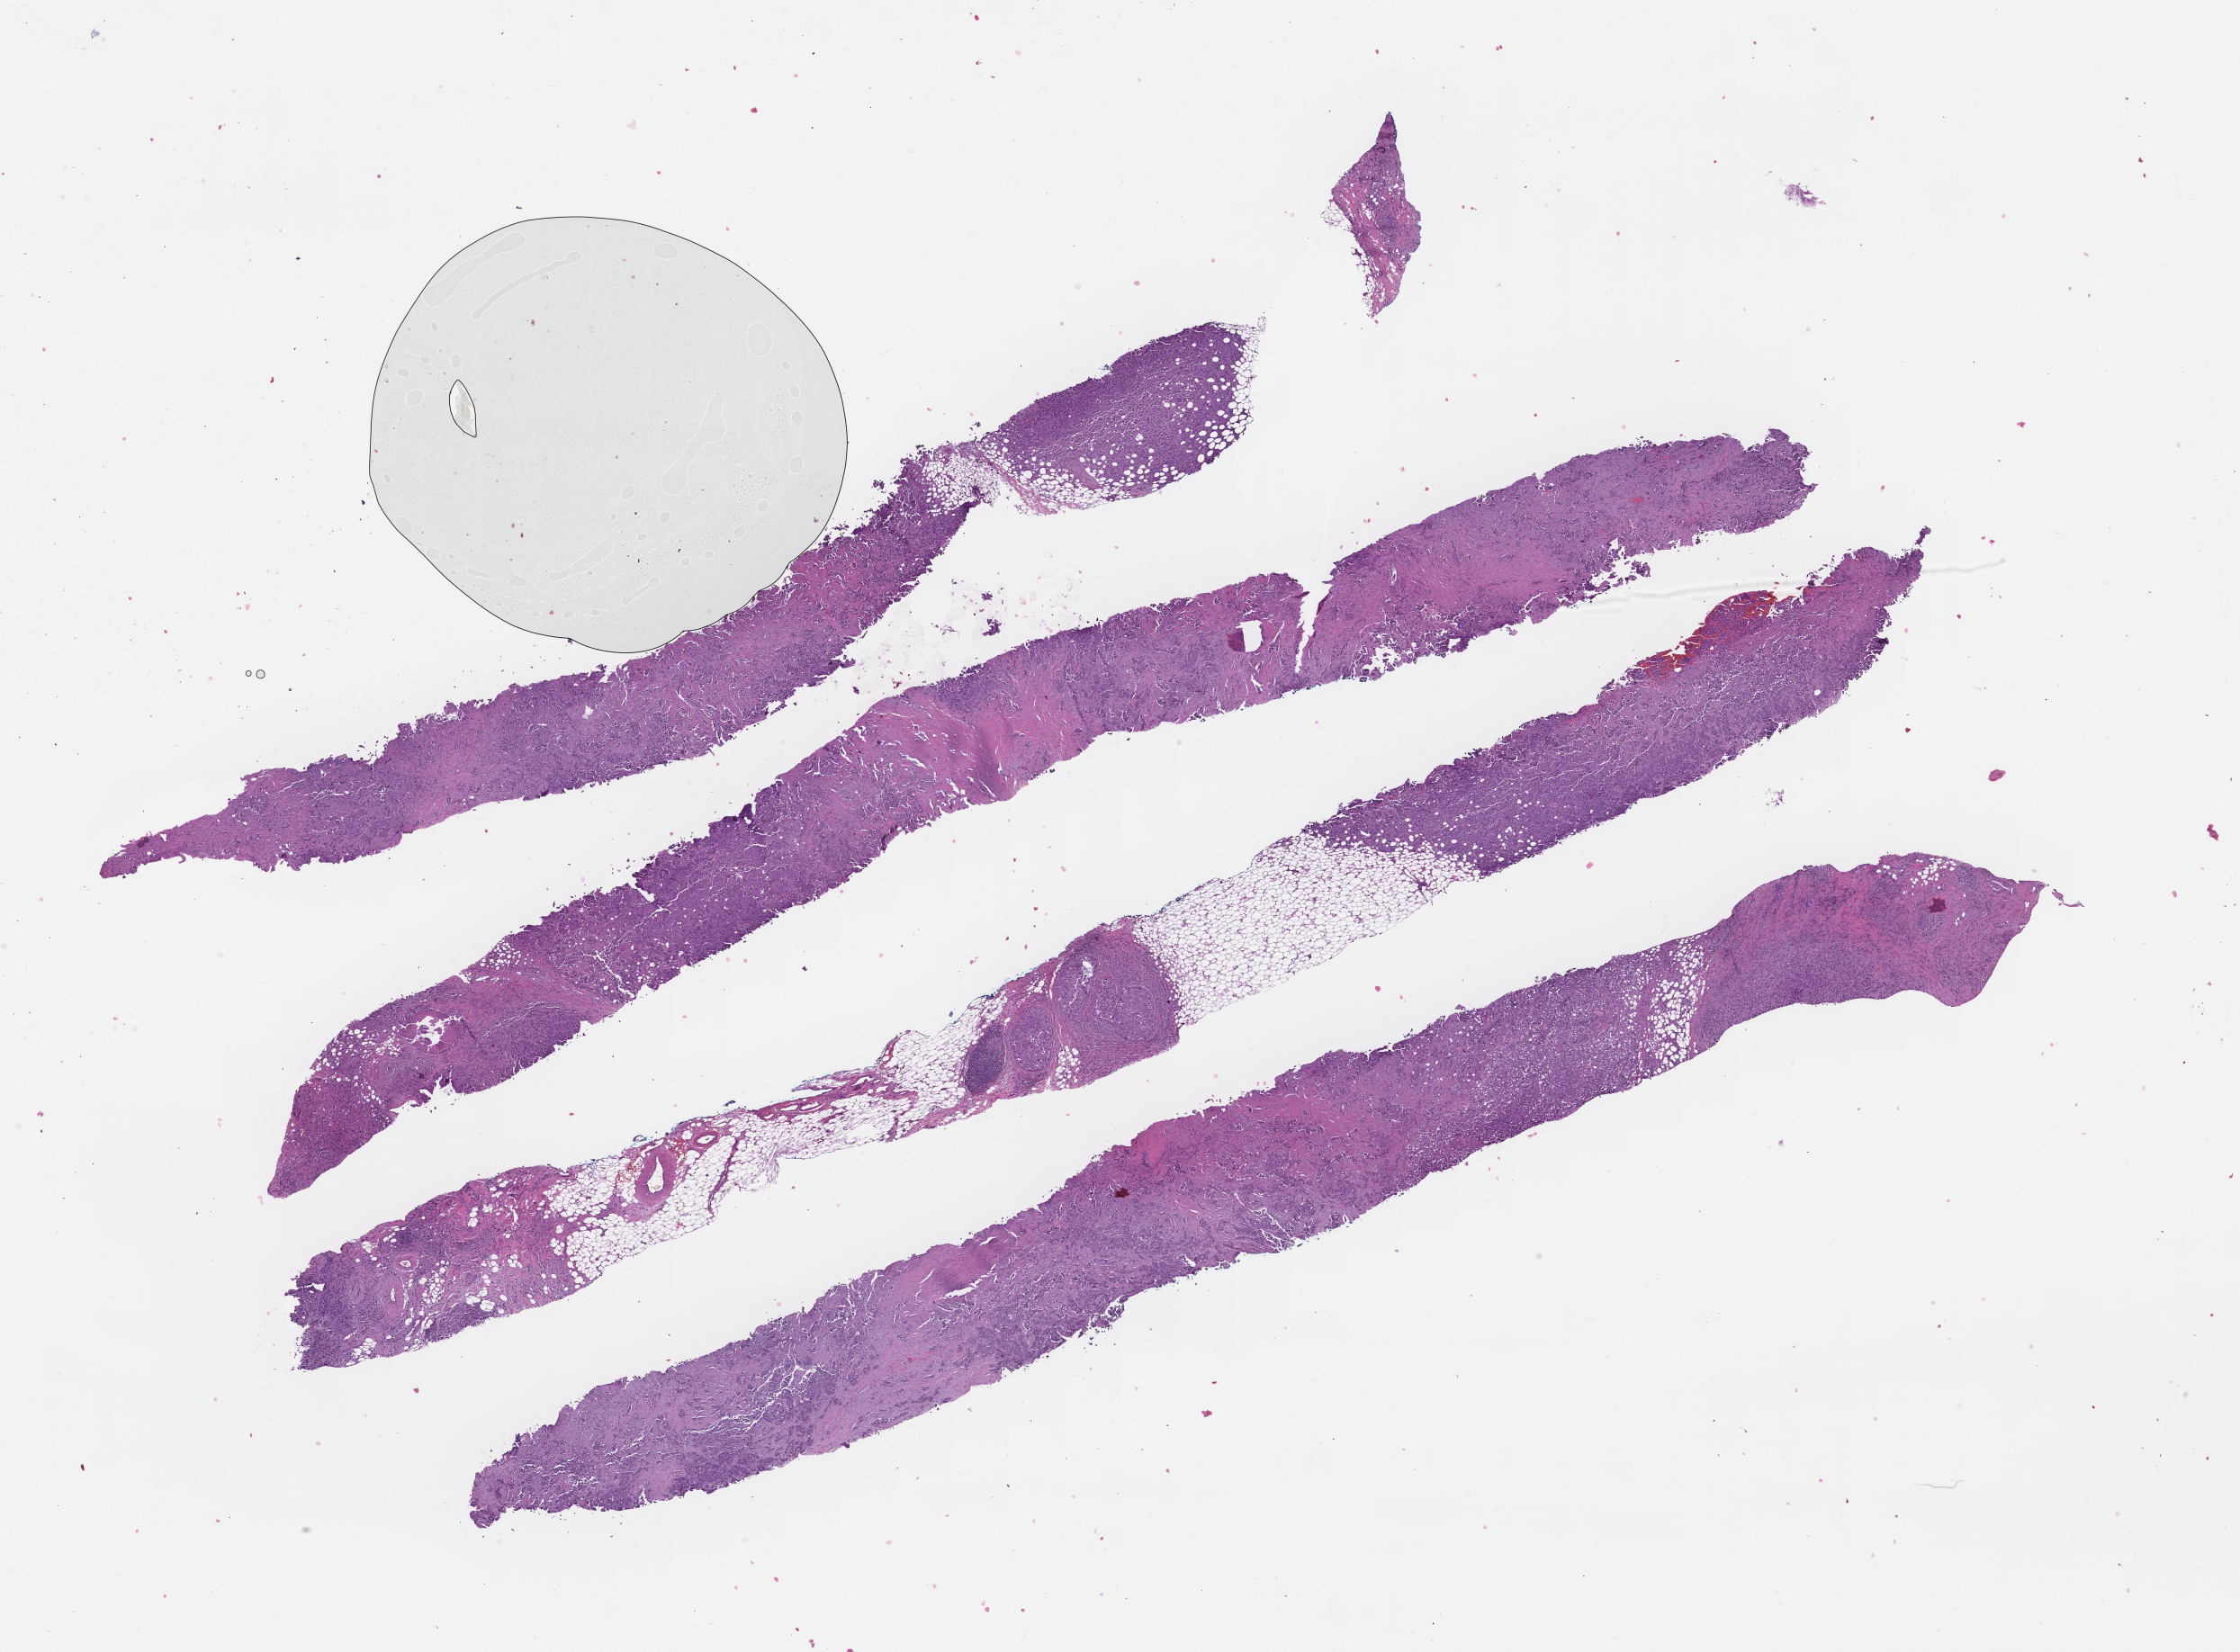
Whole-slide image, haematoxylin and eosin stain — shown as a low-resolution overview of the whole scanned area (about 20.1 x 14.8 mm); formalin-fixed paraffin-embedded section; tissue site: breast; archival tissue. Patient: female.
This section: primary tumour tissue. Diagnosis: Invasive Breast Carcinoma.